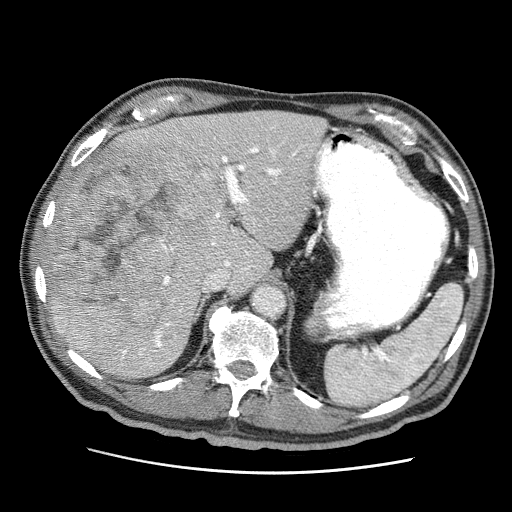
Contrast-enhanced abdominal CT (liver protocol), one axial slice; position 38 of 75 along the scan axis; soft-tissue window (W 400 / L 40 HU); 2.5 mm slice thickness; 512 × 512 image matrix. From the clinical record (not read from this slice): diagnosis: hepatocellular carcinoma (patient treated with transarterial chemoembolisation; whether this scan precedes or follows treatment is not stated here); TNM stage (as recorded): Stage-IIIA; Child-Pugh class: A; tumour nodularity: multinodular.
Outlined on this slice (semi-automatic segmentation, software-assisted and operator-edited):
- liver parenchyma outside the tumour (the mass and vessels are separate outlines, so this box may not span the whole liver): bounding box (x1, y1, x2, y2) in pixels: (46, 110, 326, 376)
- mass: (49, 136, 221, 343)
- liver vessels: (56, 118, 298, 365)